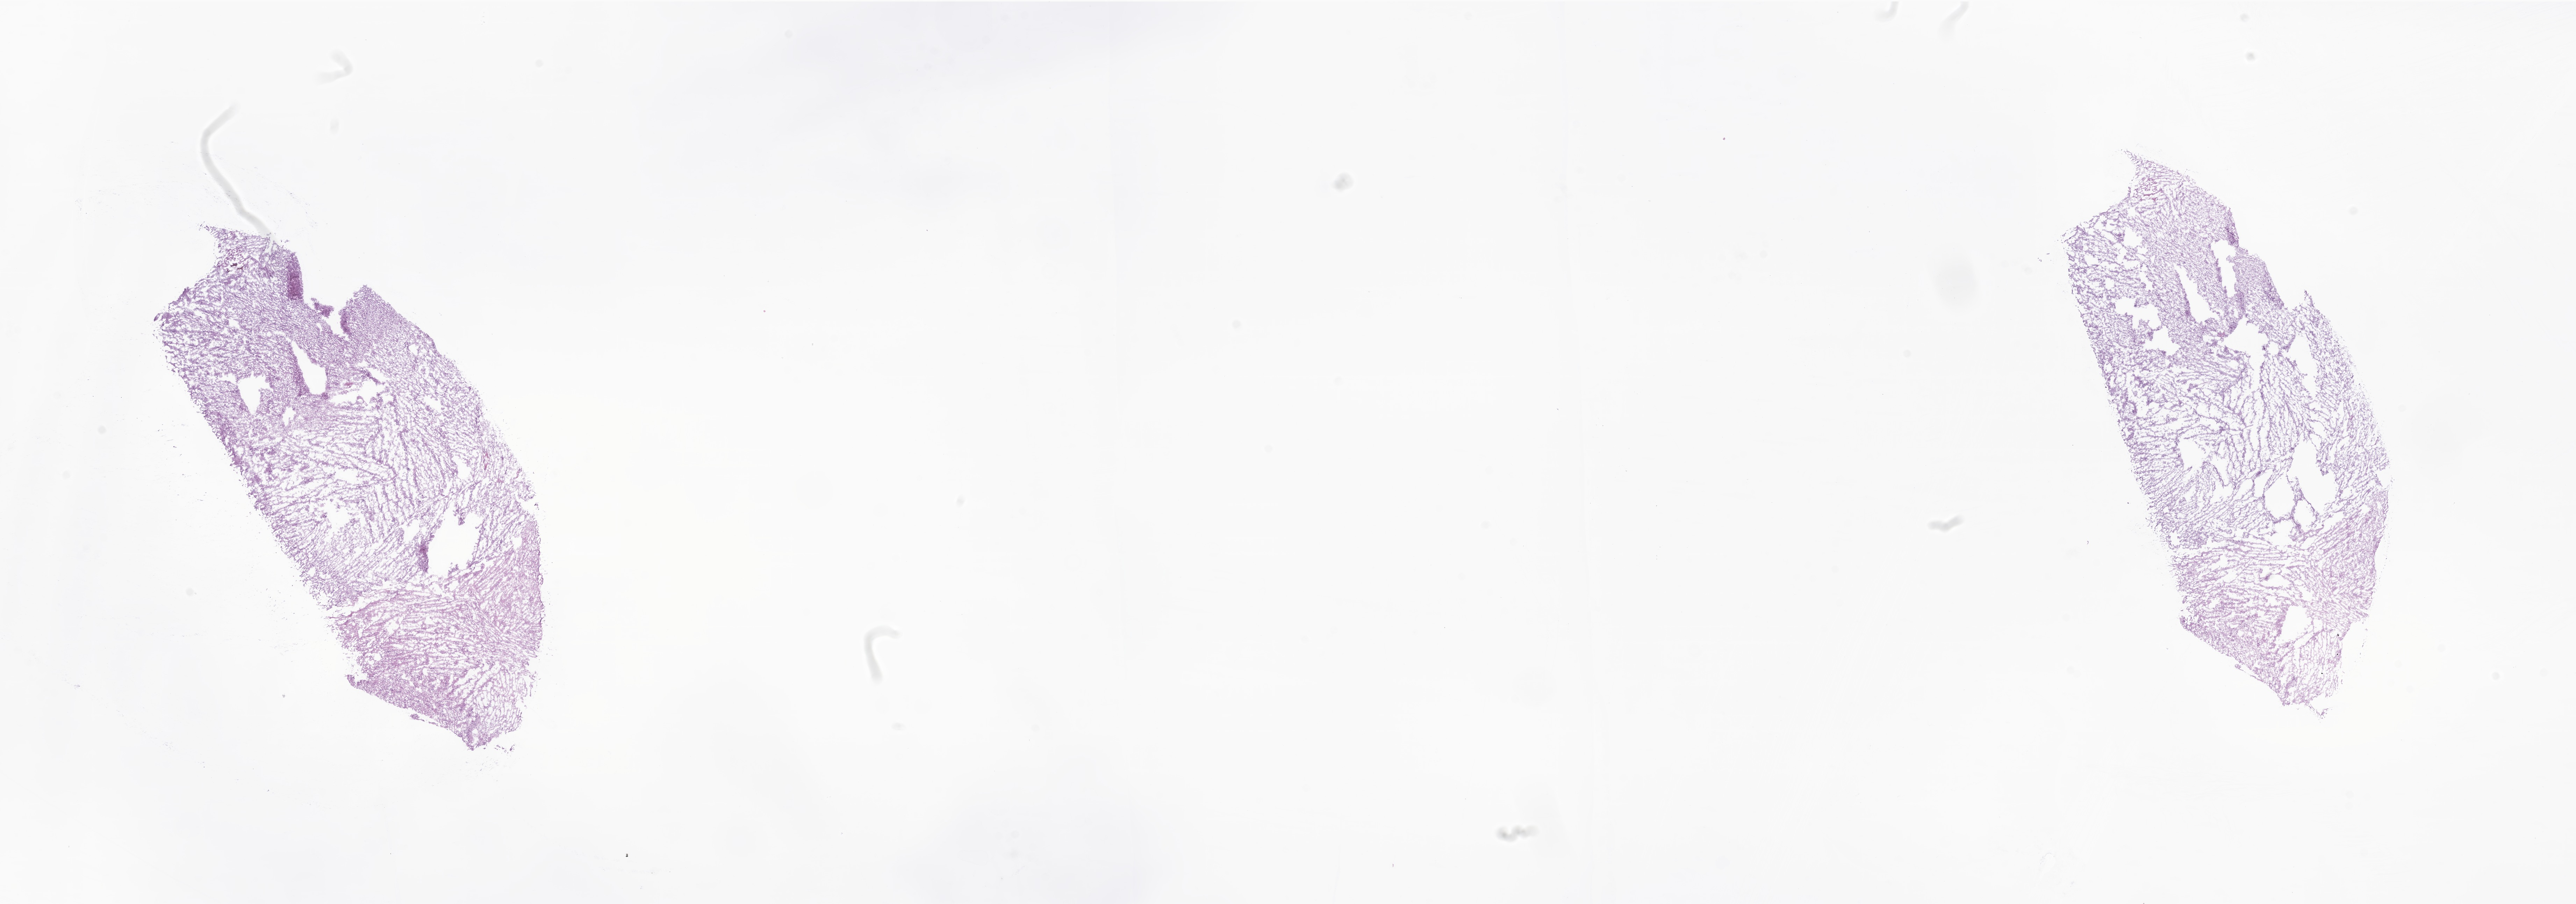
Whole-slide image, hematoxylin and eosin (H&E) stain of tumor tissue from the brain, a low-resolution overview of the entire scanned area, about 31.1 x 10.9 mm; frozen section. Patient female; age 205 months (17 years 1 month).
Recorded diagnosis: Glioma, malignant.